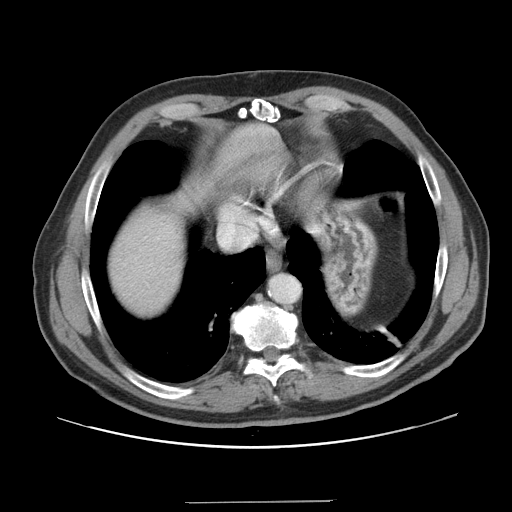
Contrast-enhanced abdominal CT, one axial slice. Position 141 of 151 along the scan axis. 120 kVp. Intravenous contrast given. Soft-tissue window (W 400 / L 40 HU). 2.5 mm slice thickness. 512 × 512 image matrix, field of view 399 × 399 mm. Male patient, age 63 years. From the clinical record (not read from this slice): diagnosis: colorectal cancer liver metastases, imaged before liver resection; multiple liver metastases: no; largest metastasis: 2.1 cm; disease in both lobes: no.
Structures marked on this image (outlined manually by an expert reader):
- hepatic veins: bounding box <221,224,255,246> (left, top, right, bottom; pixels)
- liver: <106,168,260,319>
- planned liver remnant (the part of the liver to remain after resection): <105,196,204,319>